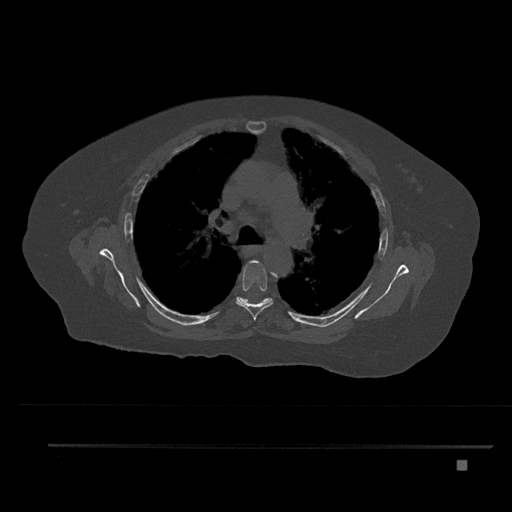
CT including the spine, one axial slice; position 563 of 797 along the scan axis; reconstruction kernel Br40s/3; 120 kVp; bone window (W 1800 / L 400 HU); 0.5 mm slice thickness; 512 × 512 image matrix. Patient: female, 76 years. From the clinical record (not read from this slice): primary cancer: lung; vertebrae with lytic lesions (as recorded): T11, L3.
Annotated regions visible in this slice (semi-automatic segmentation, software-assisted and operator-edited):
- T5 vertebra: bounding box <236,260,273,321> (left, top, right, bottom; pixels)
- T6 vertebra: <236,297,272,304>